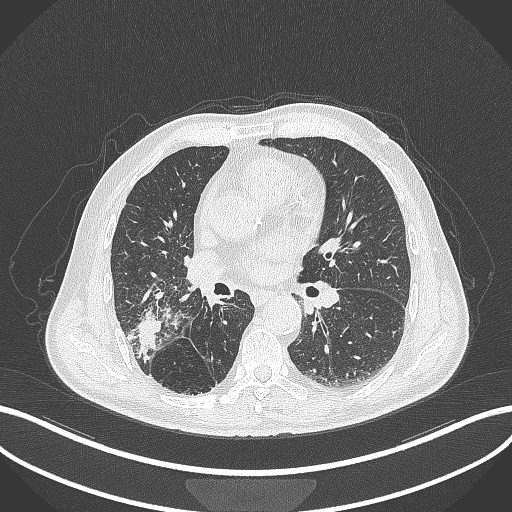
Chest CT, one axial slice. Slice 215 of 429 in the series (ordered by position). Lung window (W 1500 / L -600 HU). 1 mm slice thickness. 512 × 512 image matrix, field of view 400 × 400 mm. Patient: male, 72 years. Case-level facts recorded for this patient, not image findings: clinical TNM (as recorded): T3 N2 M0.
Outlined on this slice (rectangle marked by the reading radiologist):
- lung tumour (recorded histology: adenocarcinoma): bounding box [x1, y1, x2, y2] px = [130, 310, 165, 361]